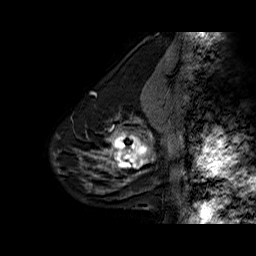
Breast MRI (dynamic contrast-enhanced), one sagittal slice. Slice 19 of 60 in the series (ordered by position). Dynamic contrast-enhanced series, time point 2 of 6 at this slice position (early post-contrast). 1.5 T. TE 6.3 ms, TR 32.5 ms. 4 mm slice thickness. 256 × 256 image matrix, field of view 200 × 200 mm. Female patient. From the clinical record (not read from this slice): setting: breast cancer imaged before/during neoadjuvant chemotherapy; receptor status: triple-negative.
Structures marked on this image (semi-automatic segmentation, software-assisted and operator-edited):
- analysis volume of interest (the breast-tissue region the enhancement analysis was run in; not a lesion): bounding box (x1, y1, x2, y2) in pixels: (108, 126, 154, 177)
- tumour enhancement mask (voxels above the 100 % enhancement threshold inside the analysis volume of interest): (108, 131, 152, 174)